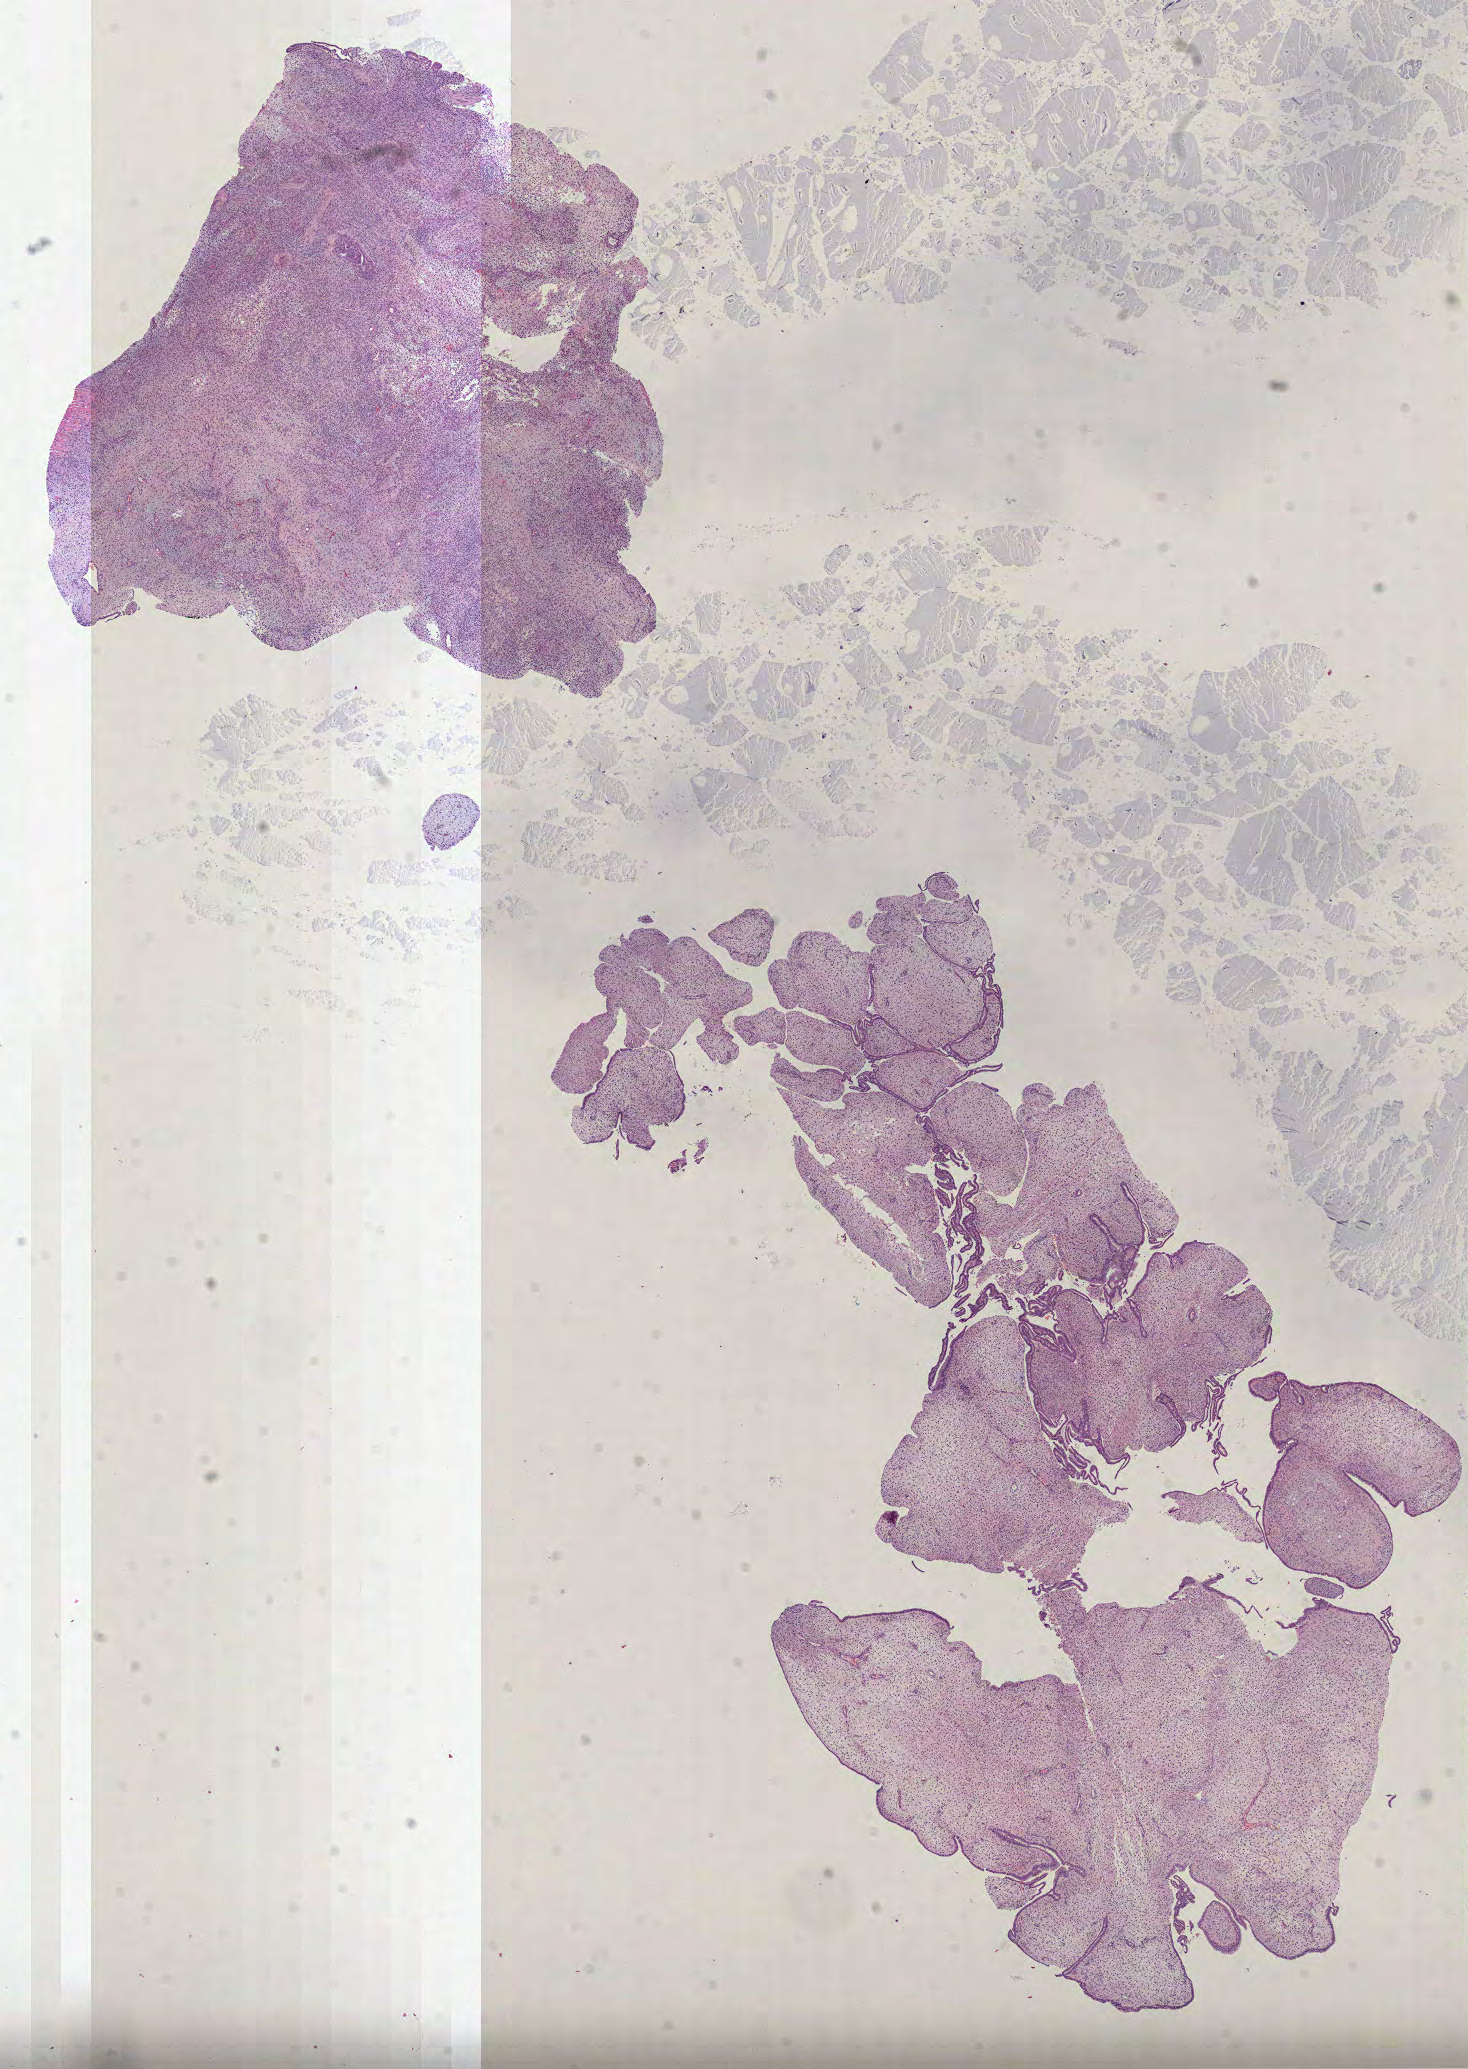
Whole-slide histology image, H&E, whole scanned area (about 11.8 x 16.7 mm) shown as a low-resolution overview, formalin-fixed paraffin-embedded (FFPE) diagnostic section, sample: primary tumour, breast. Female, age 88 years at initial diagnosis.
• AJCC pathologic stage: IB (7th edition)
• lymph nodes positive (case pathology): 1 of 2 examined
• histologic diagnosis: Phyllodes tumor, malignant
• laterality: right